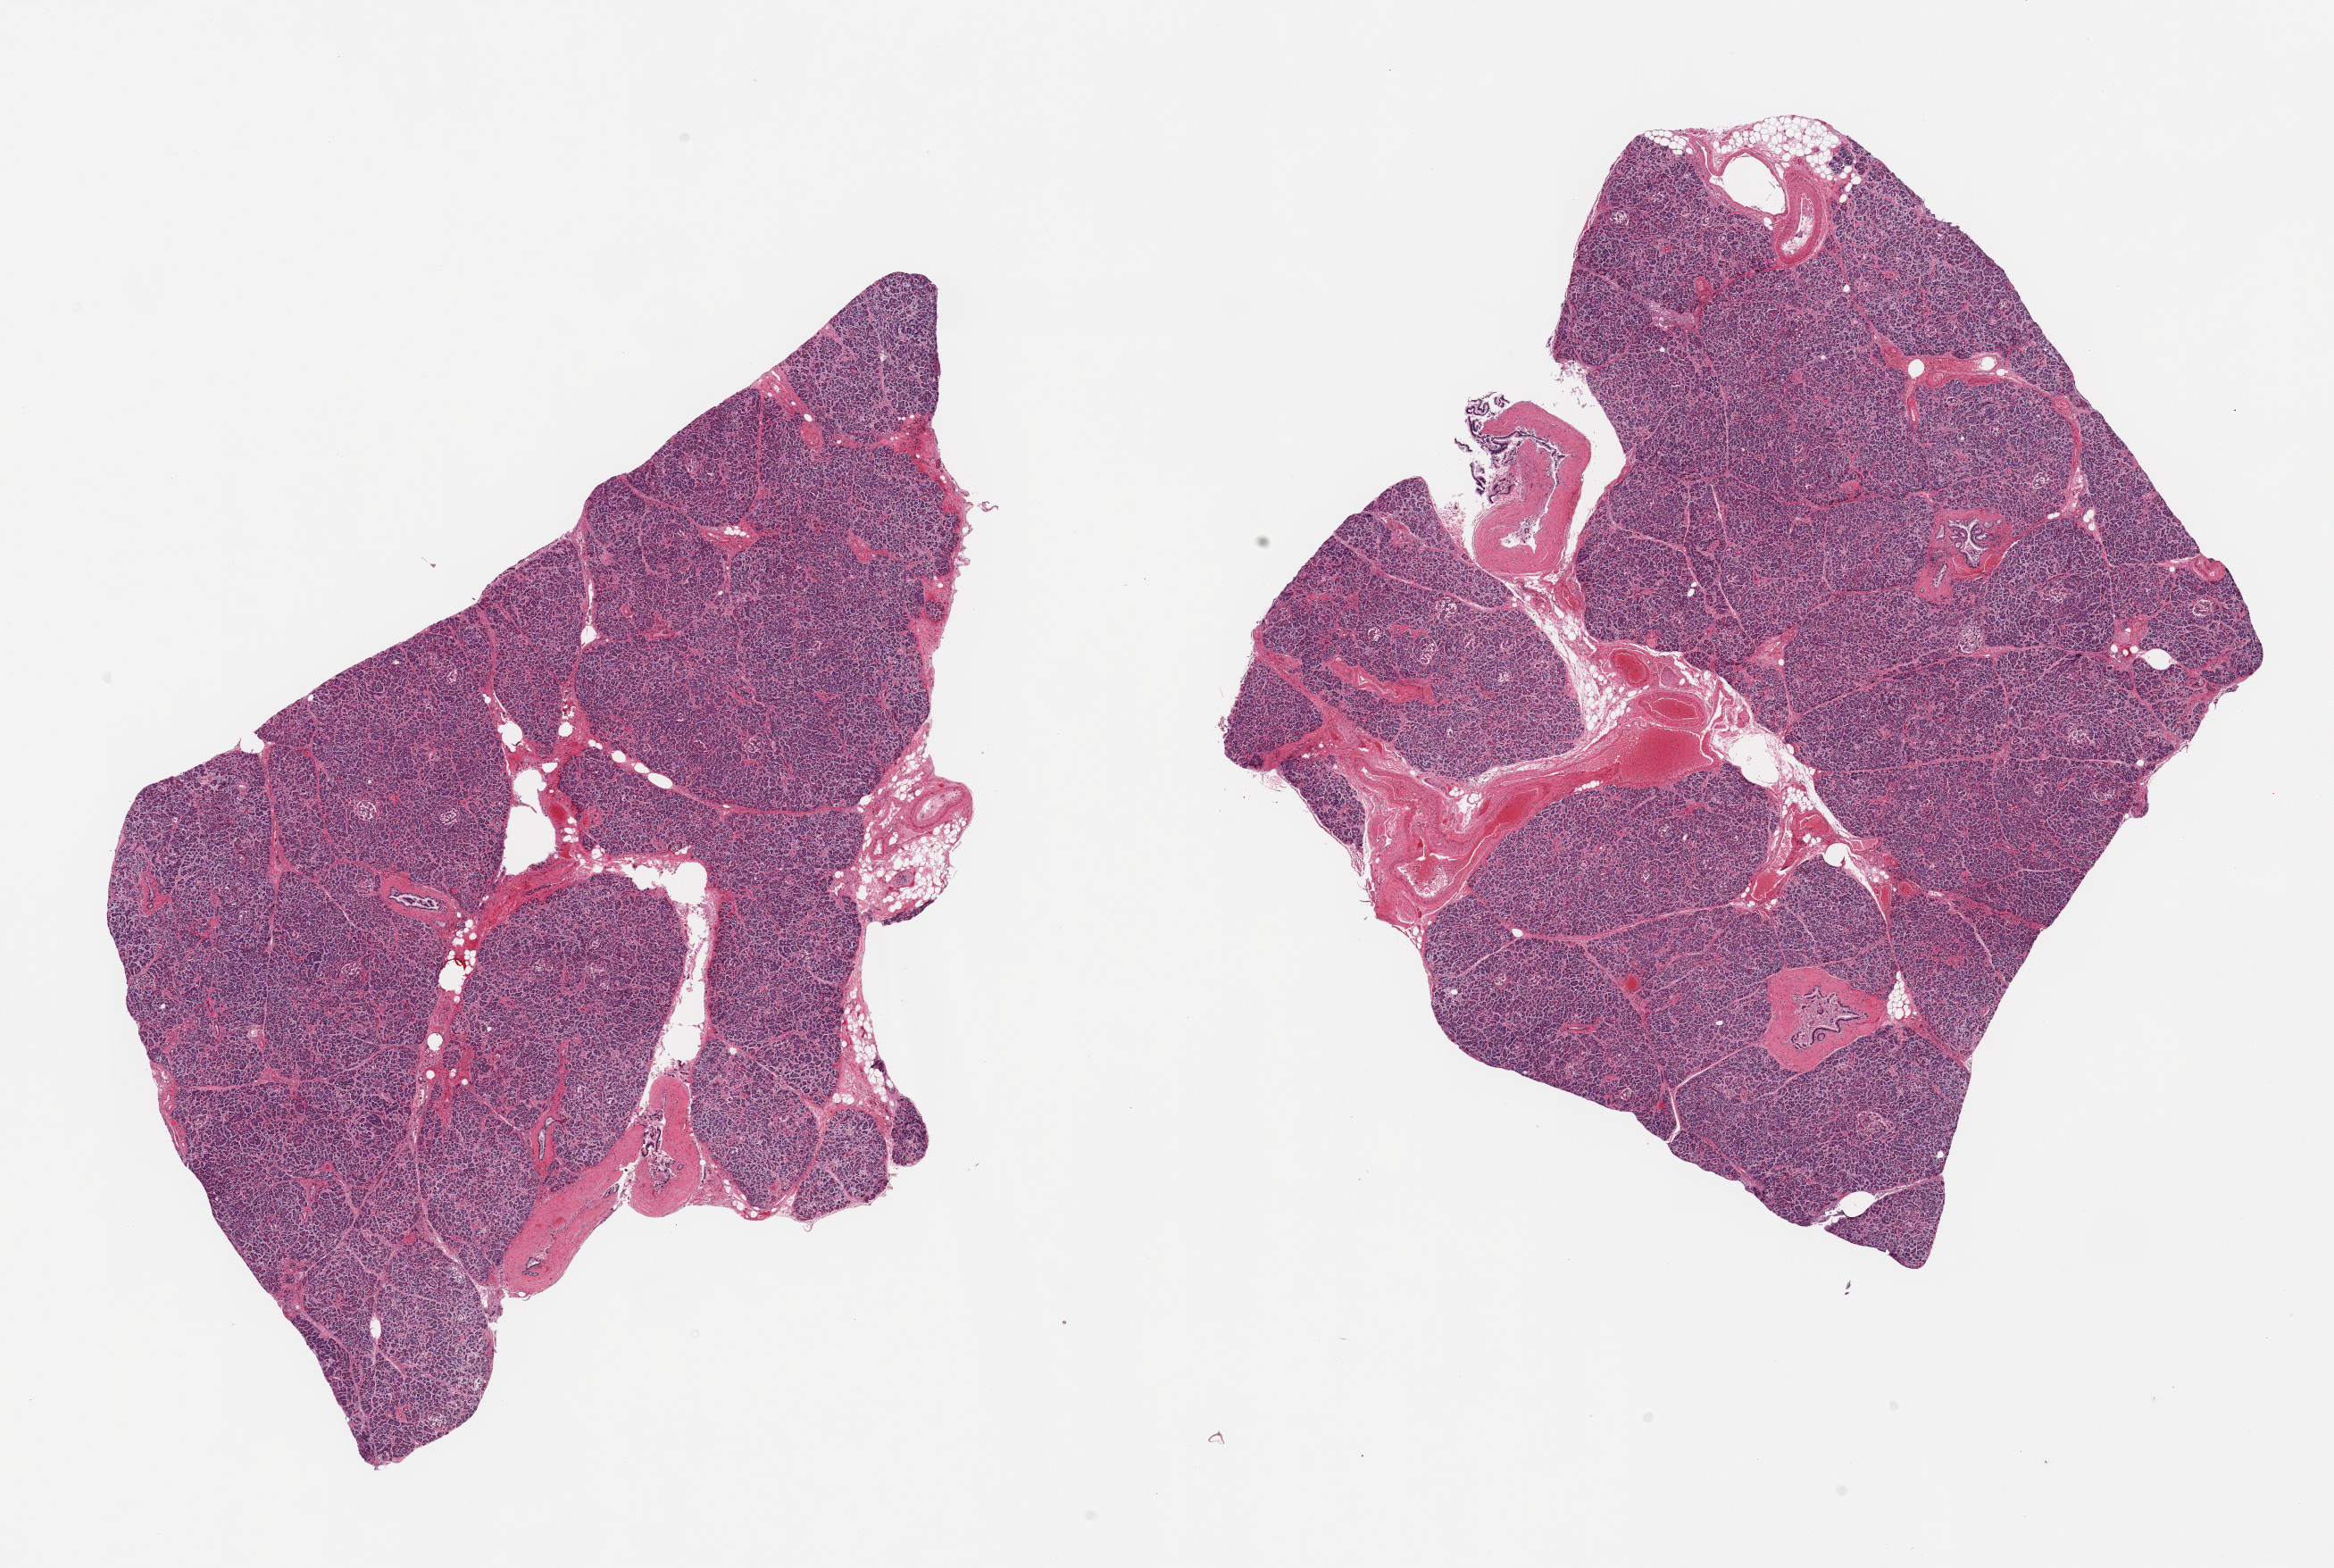
Digitized H&E-stained section, brightfield, a low-resolution overview of the entire scanned area, about 20.7 x 13.9 mm, PAXgene-fixed, paraffin-embedded tissue, sampled site (target tissue): pancreas, donor tissue sample. Donor: male.
Pathologist's review note for this sample: 2 pieces; some fibrosis, mild chronic inflammation, PanIN-1.